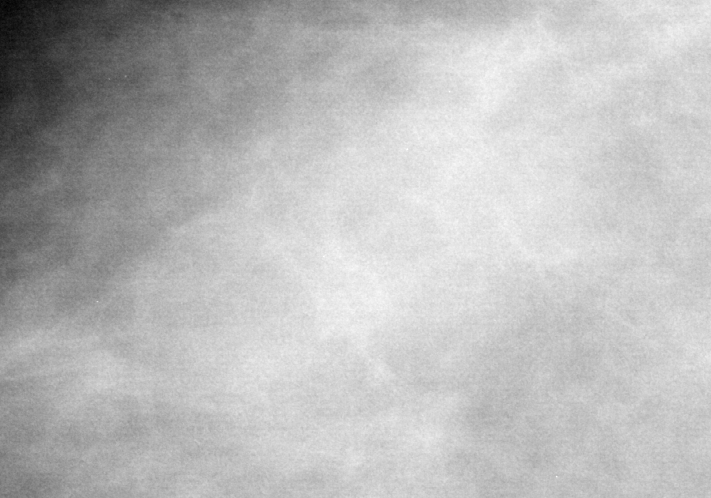
Cropped region of a digitized screen-film mammogram centred on a radiologist-marked abnormality, right breast, MLO view.
Mass, shape asymmetric breast tissue; BI-RADS assessment category 2; subtlety rating 4 on a 1 (subtle) to 5 (obvious) scale; benign; no additional work-up was recommended (benign without callback).